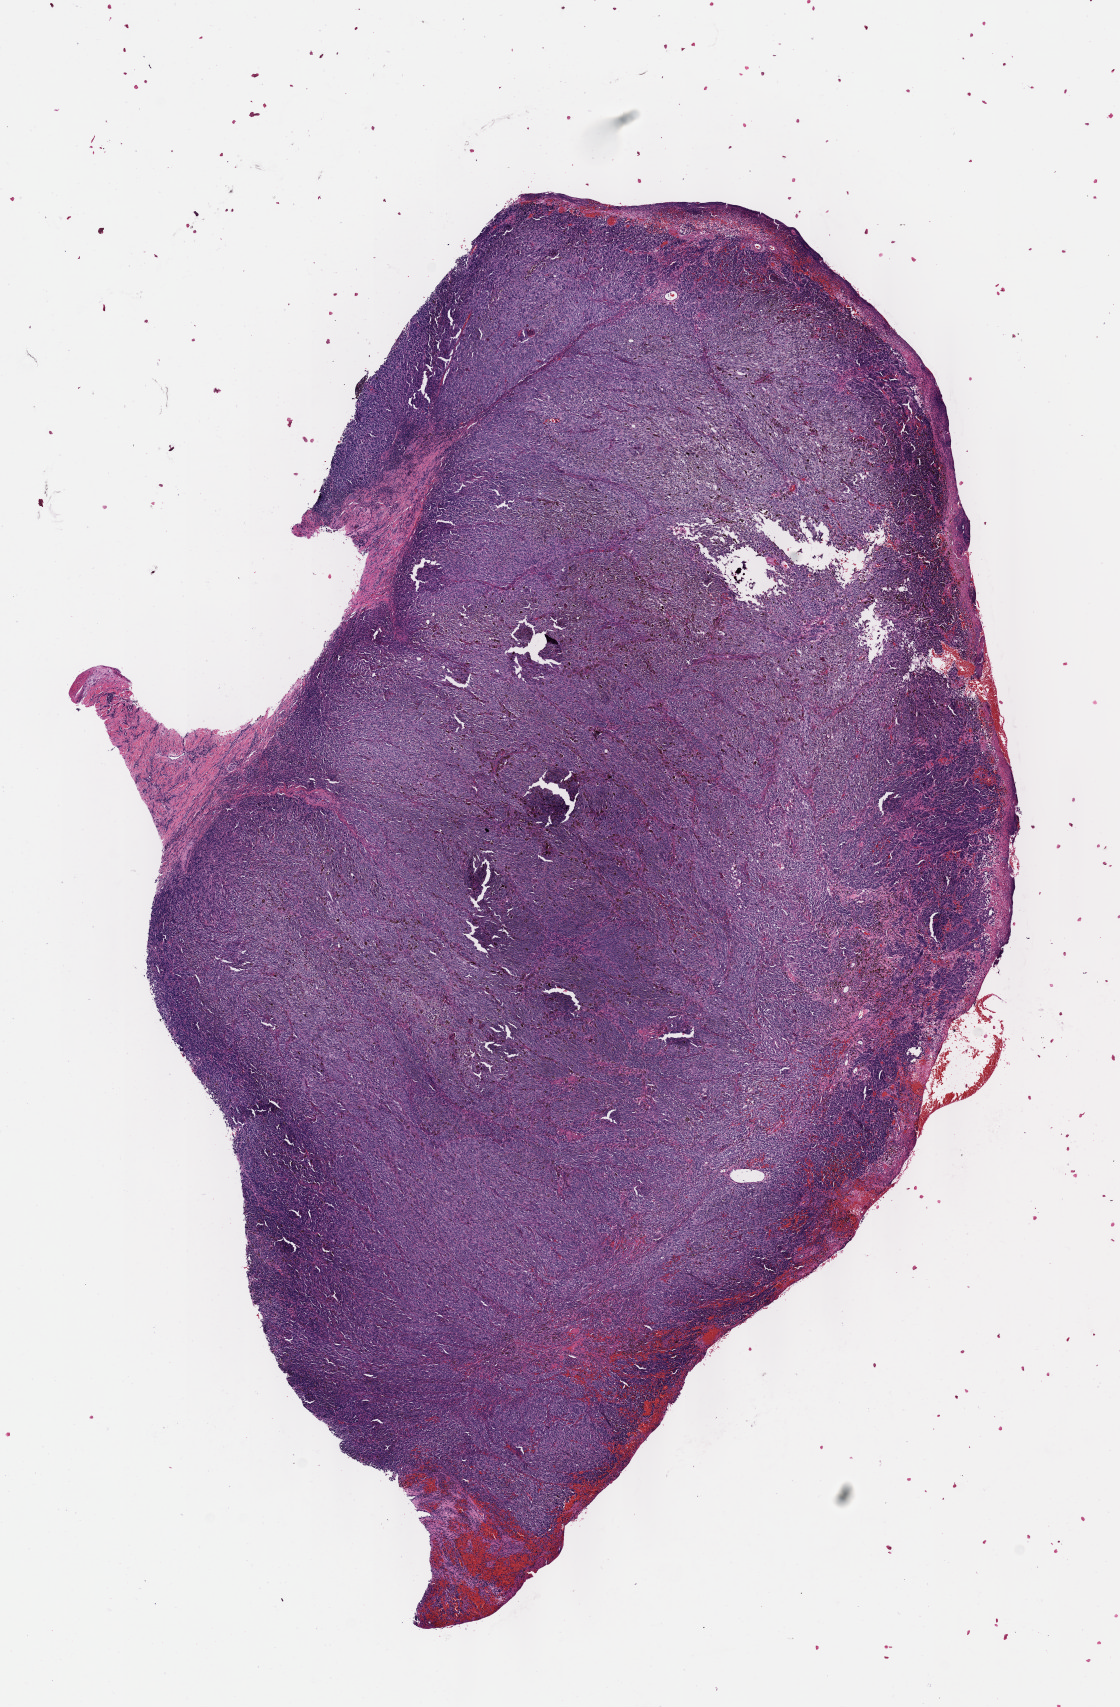
Whole-slide histology image, H&E-stained, shown as a low-resolution overview of the whole scanned area (about 9.1 x 13.8 mm). Formalin-fixed paraffin-embedded (FFPE) diagnostic section. Sample: primary tumour, skin. Patient: male, age at initial diagnosis 61 years.
• diagnosis: Epithelioid cell melanoma
• AJCC pathologic stage: IIC (7th edition)
• TNM: T4b N0 M0